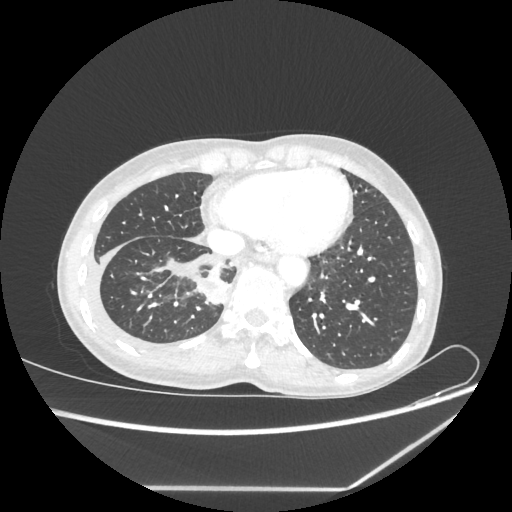
Chest CT, one axial slice. Slice 63 of 237 in the series (ordered by position). 80 kVp. Lung window (W 1500 / L -600 HU). 1.25 mm slice thickness. 512 × 512 image matrix. Female patient, age 59 years. From the clinical record (not read from this slice): clinical TNM (as recorded): T1c N1 M1.
Annotated regions visible in this slice (bounding box drawn by a radiologist):
- lung tumour (recorded histology: adenocarcinoma): box from (x=192, y=273) to (x=229, y=306) px